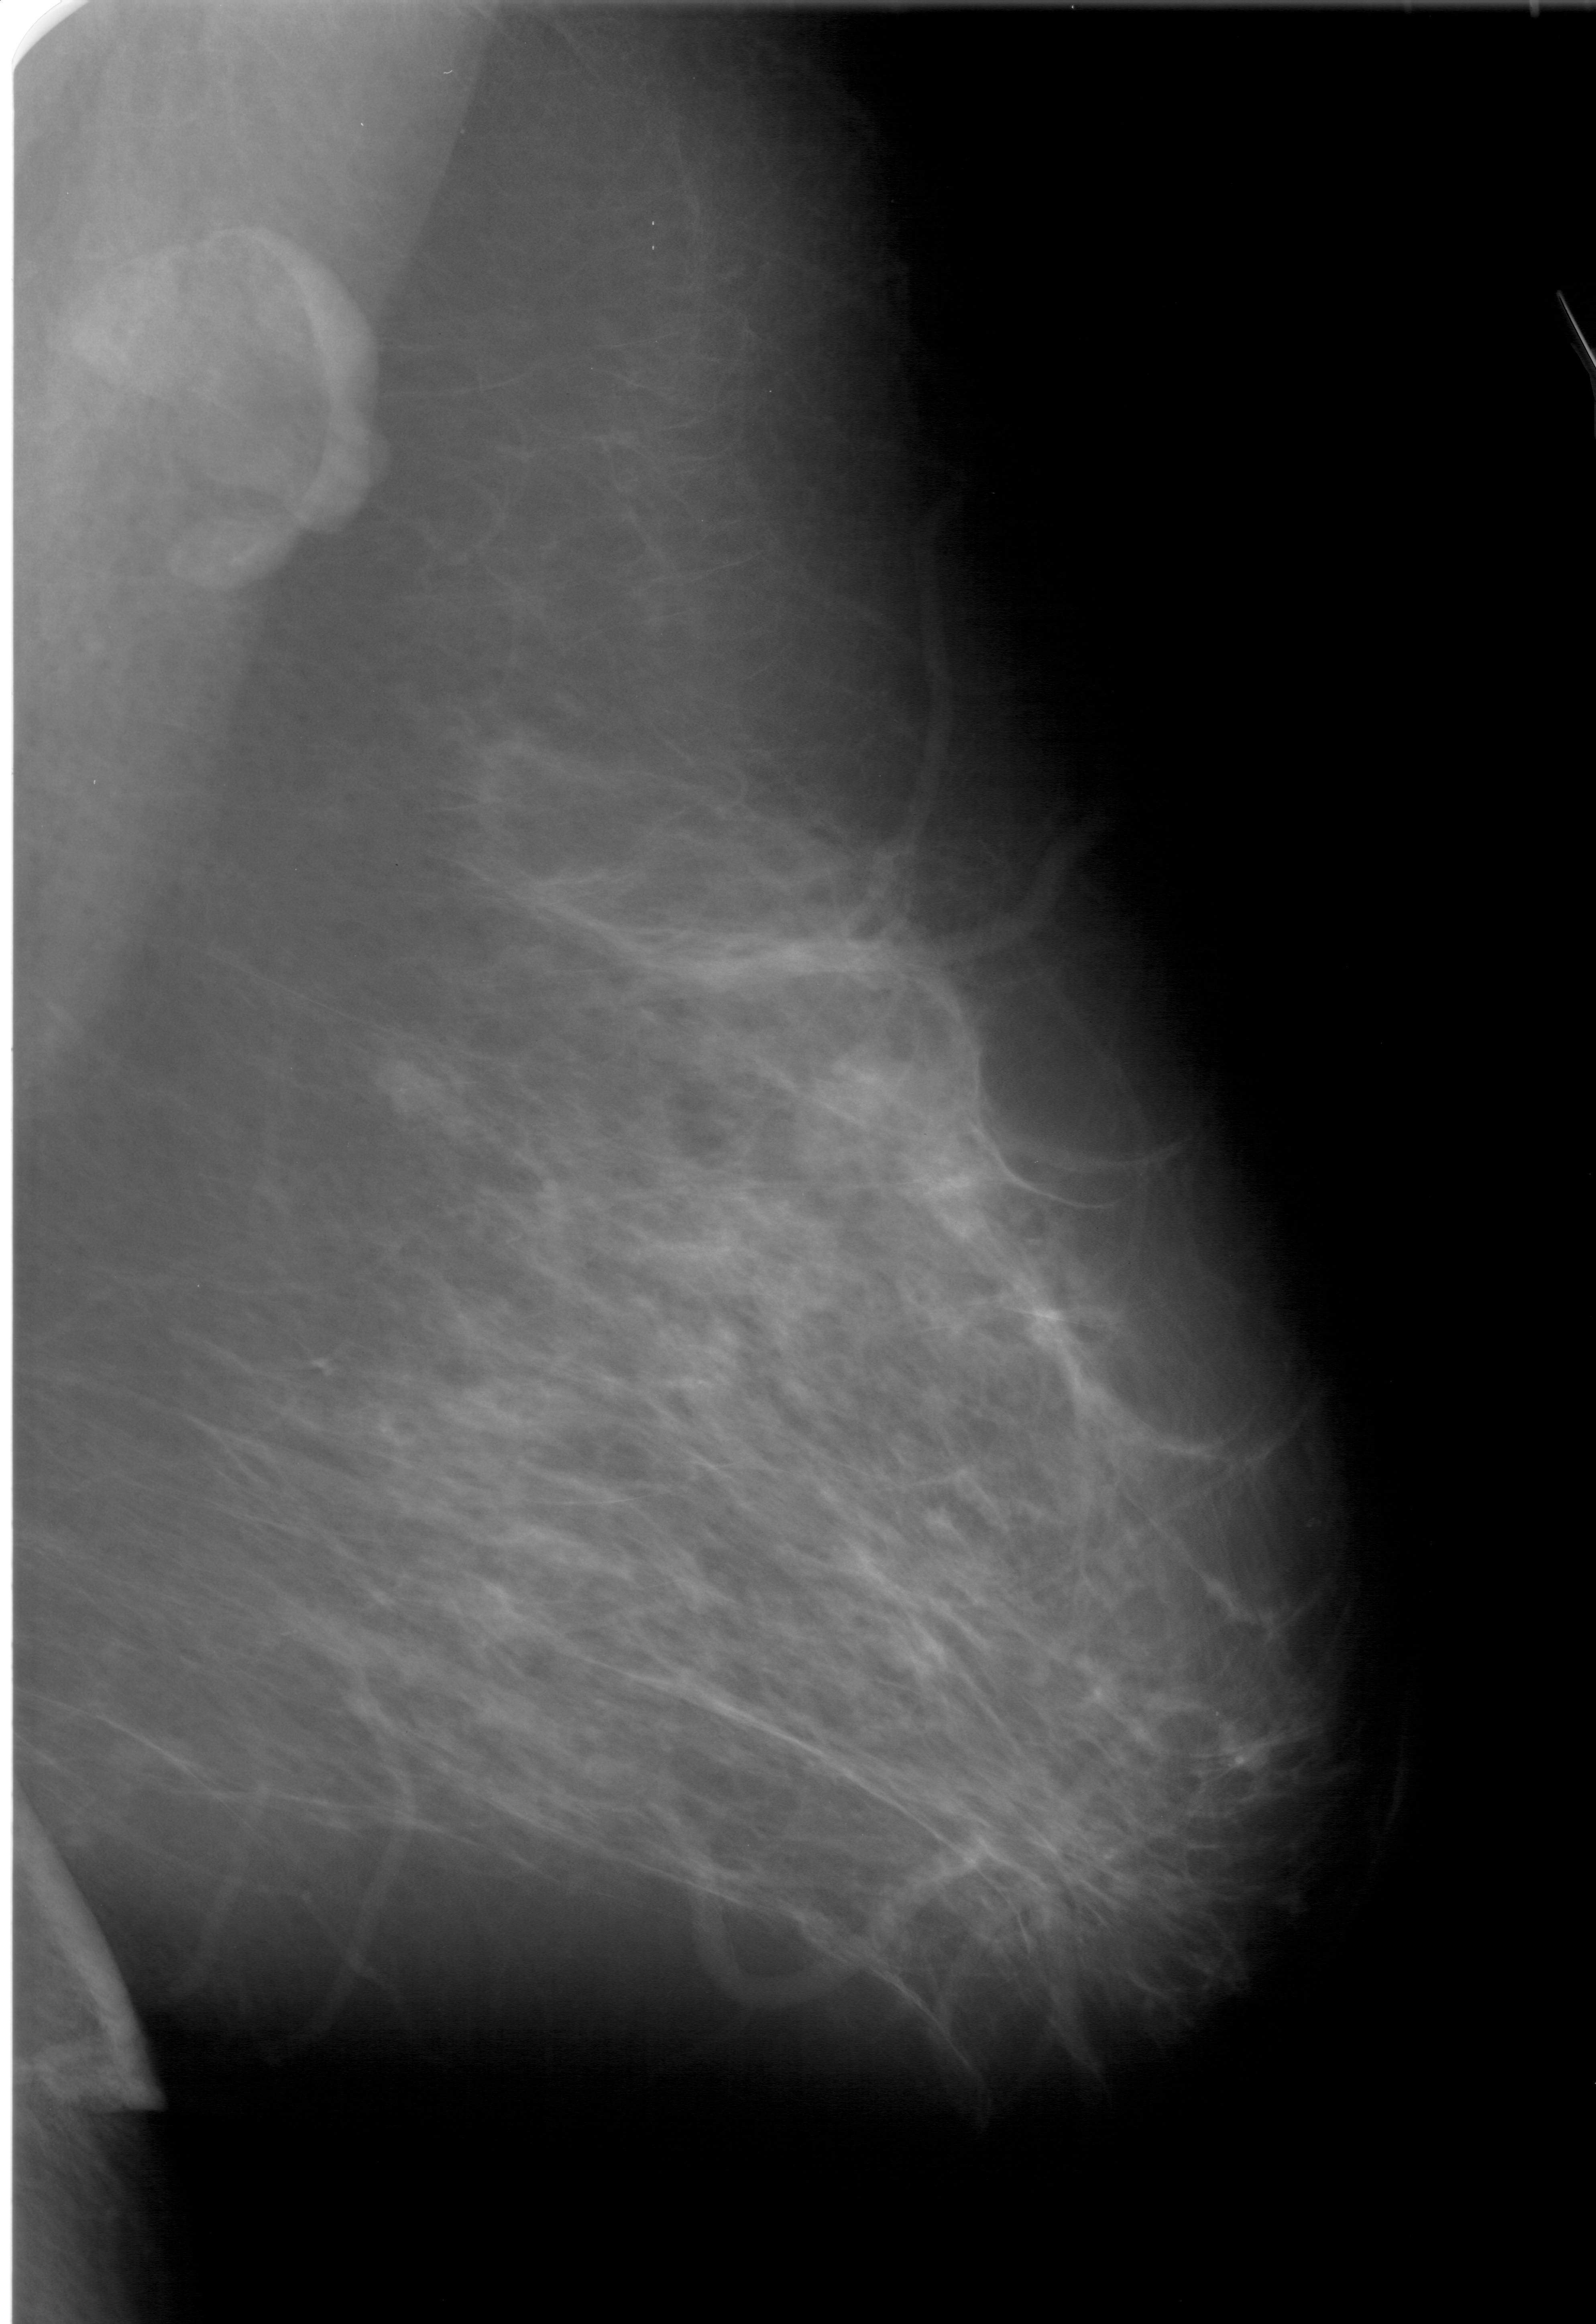
Scanned film-screen mammogram; right breast; mediolateral oblique (MLO) view; BI-RADS breast density category 3 (scale 1–4).
- Finding: mass, shape lobulated, margins ill defined; BI-RADS assessment category 4; subtlety rating 4 on a 1 (subtle) to 5 (obvious) scale; pathology result (as recorded, not read from the image): malignant.